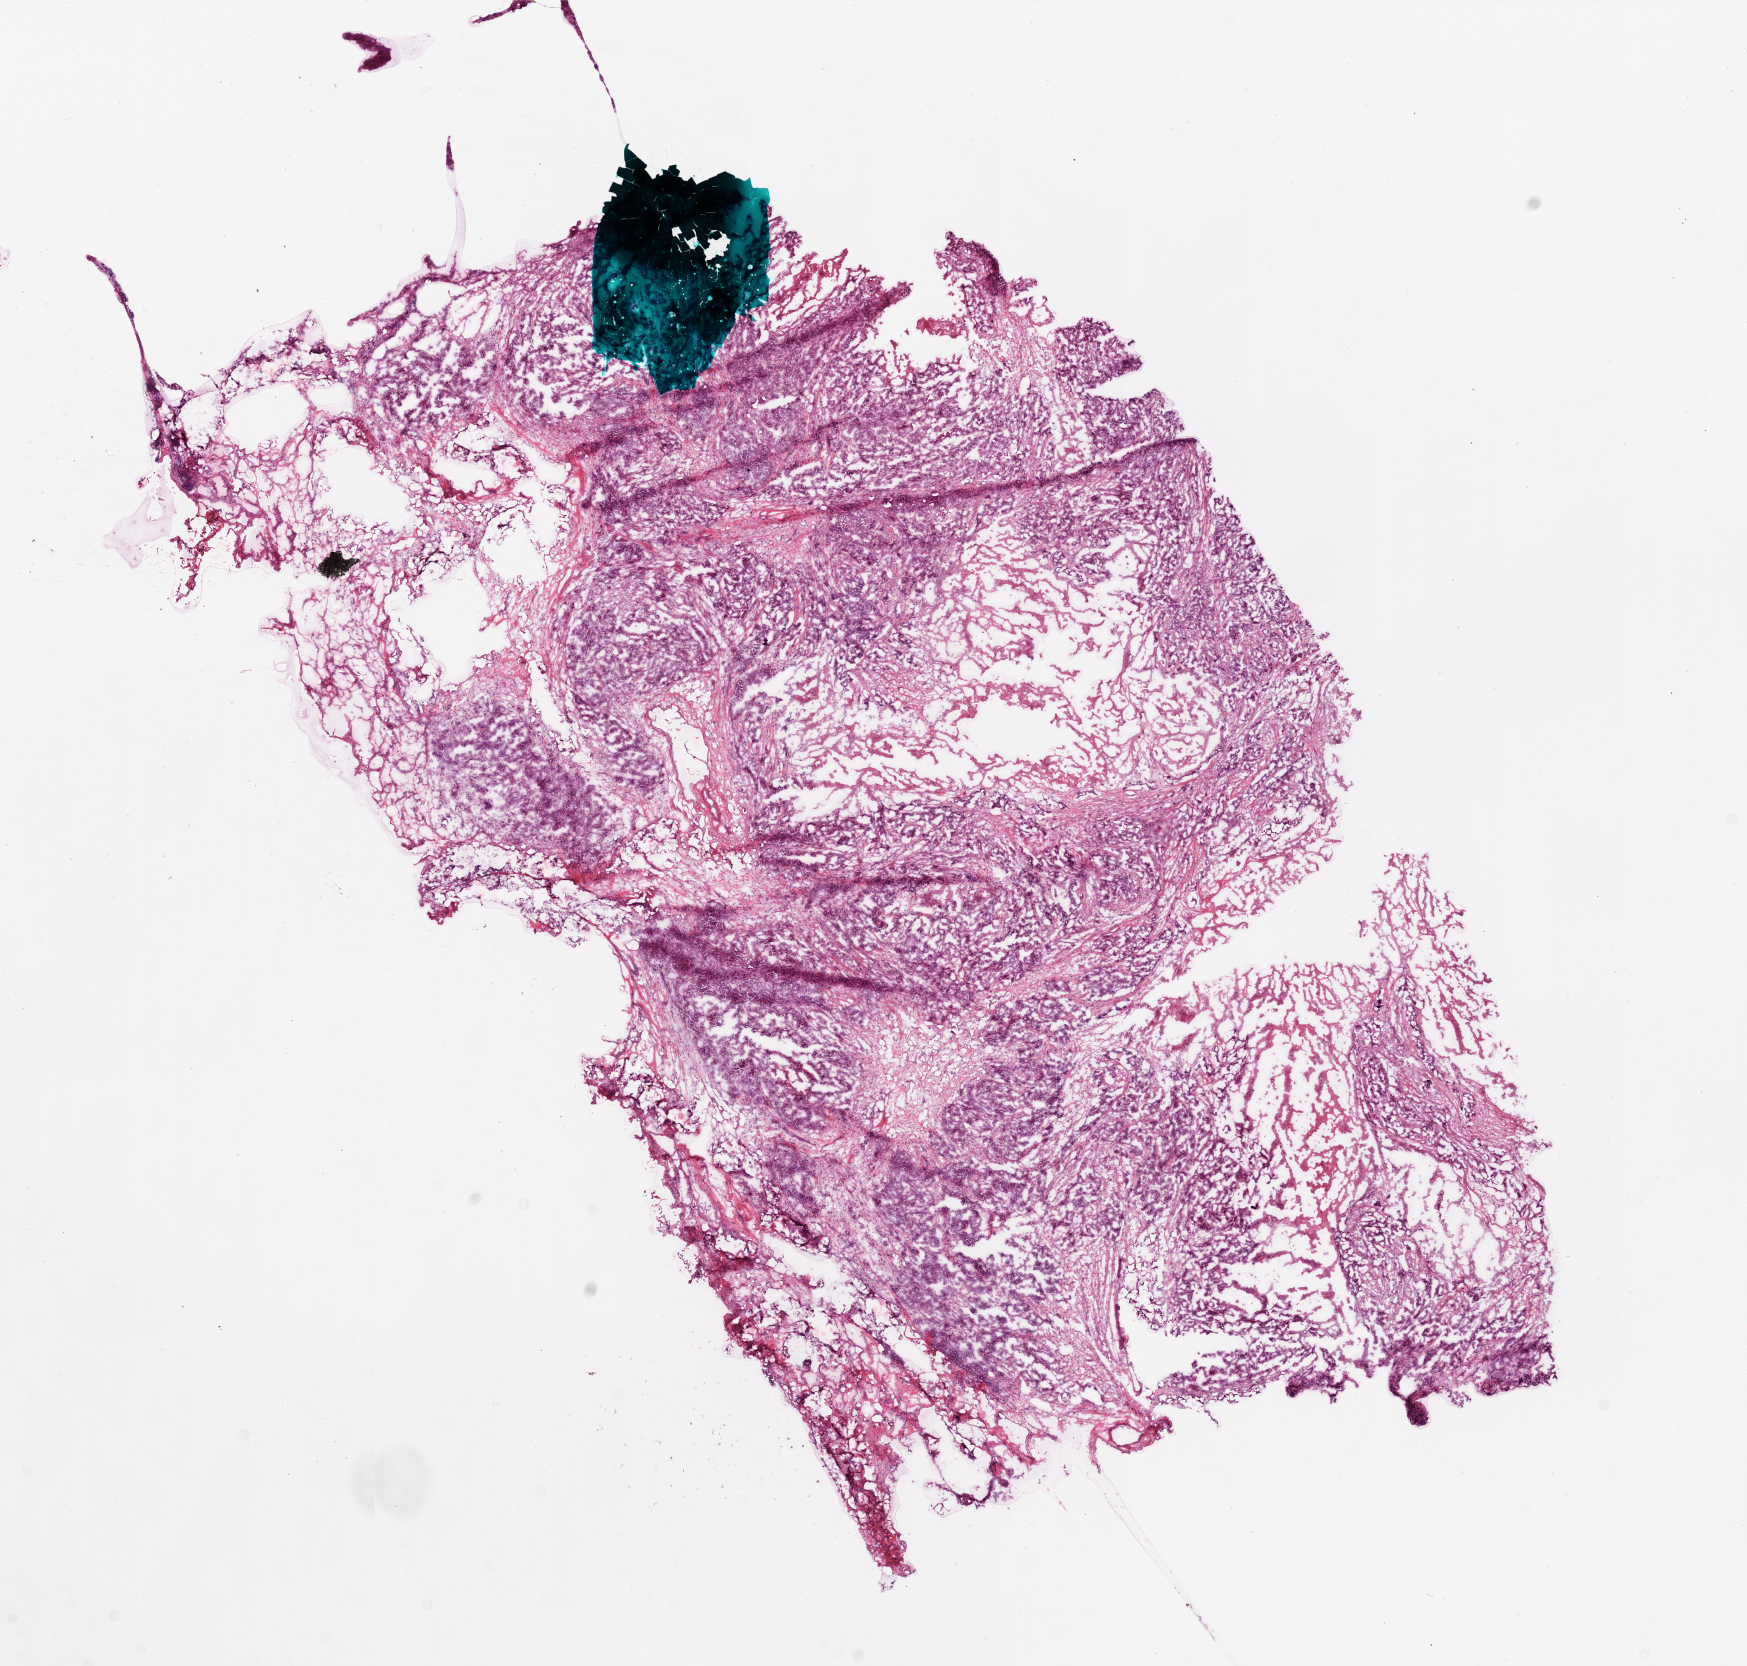
Digitized Hematoxylin and eosin (H&E) stained tissue section (whole slide), low-resolution overview of the scanned area, about 14.0 x 13.3 mm. Frozen section from the bottom of the tissue portion. Sample: primary tumour, ovary. Female patient; age at initial diagnosis 58 years. Histologic grade: G3 (poorly differentiated). Composition of this section per pathologist review: tumour nuclei 80%, normal cells 0%, stromal cells 0%, necrosis 20%.
FIGO stage: IIIC. Diagnosis: Serous cystadenocarcinoma, NOS.